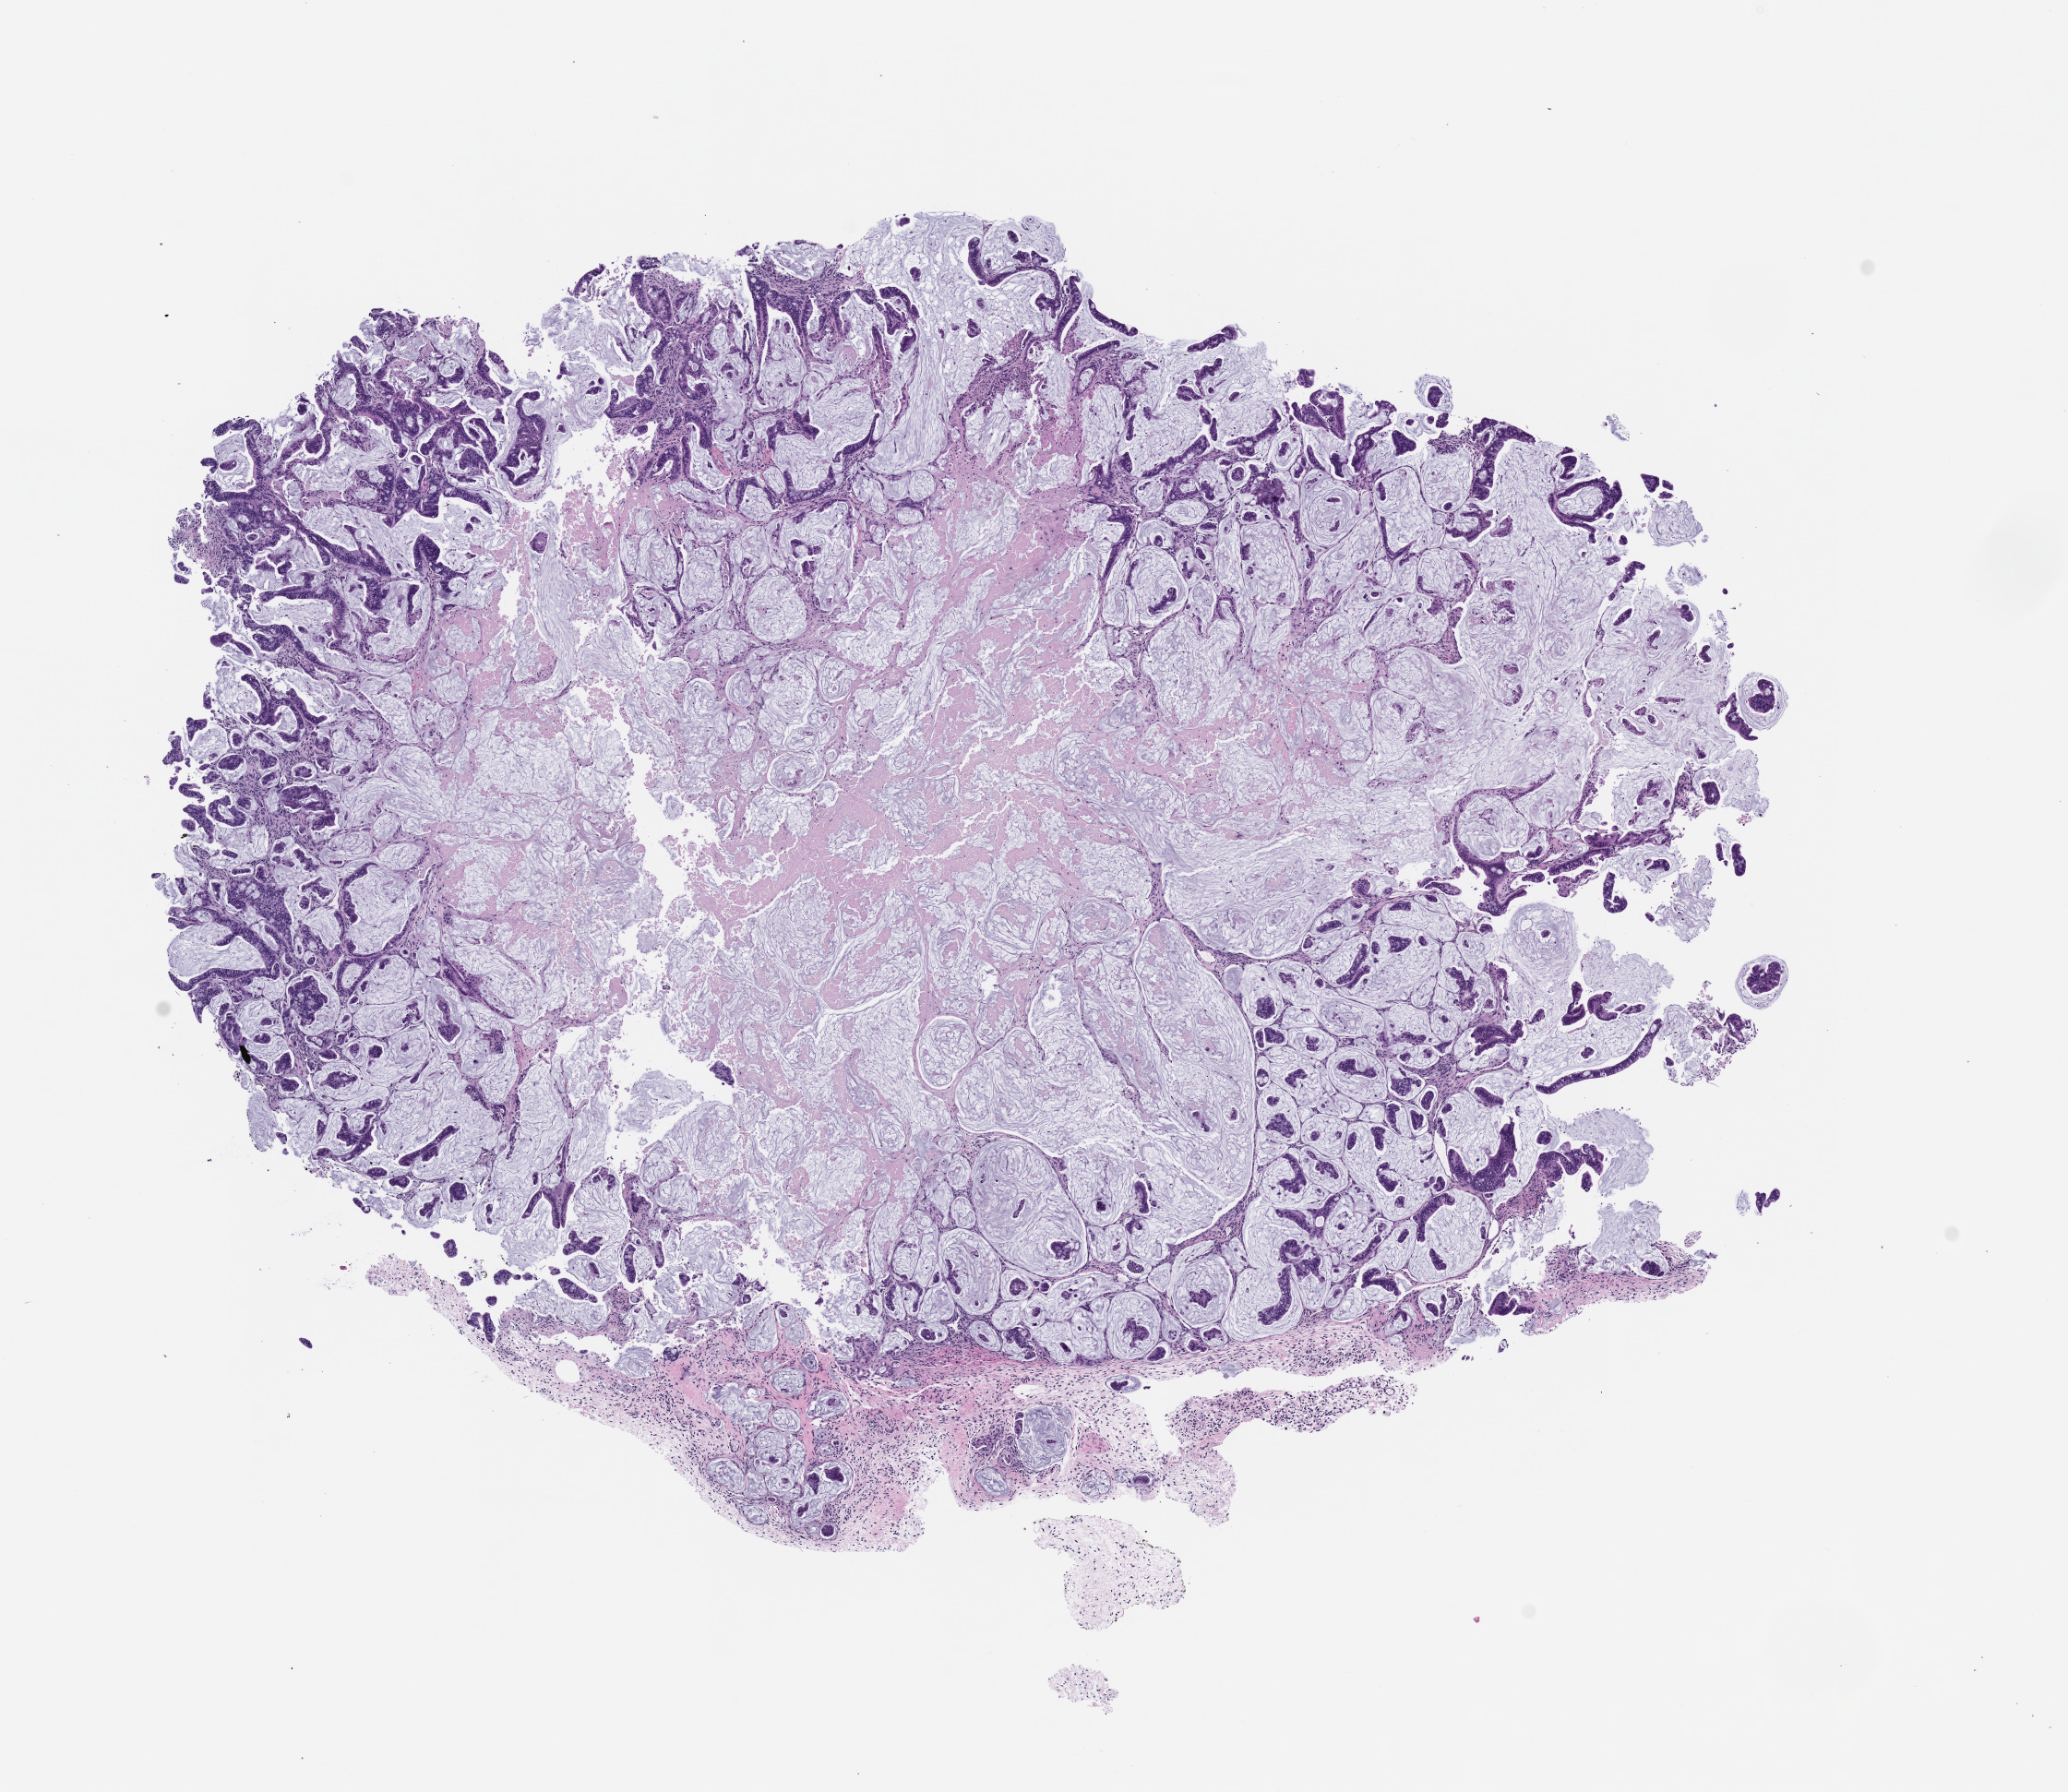
Haematoxylin and eosin whole-slide image of a patient-derived xenograft (PDX) tumor grown in a mouse, passage 3 — whole scanned area (about 9.0 x 7.8 mm) shown as a low-resolution overview; formalin-fixed, paraffin-embedded (FFPE) tissue; tumor site category: rectum.
Originating patient diagnosis: Rectal Adenocarcinoma.